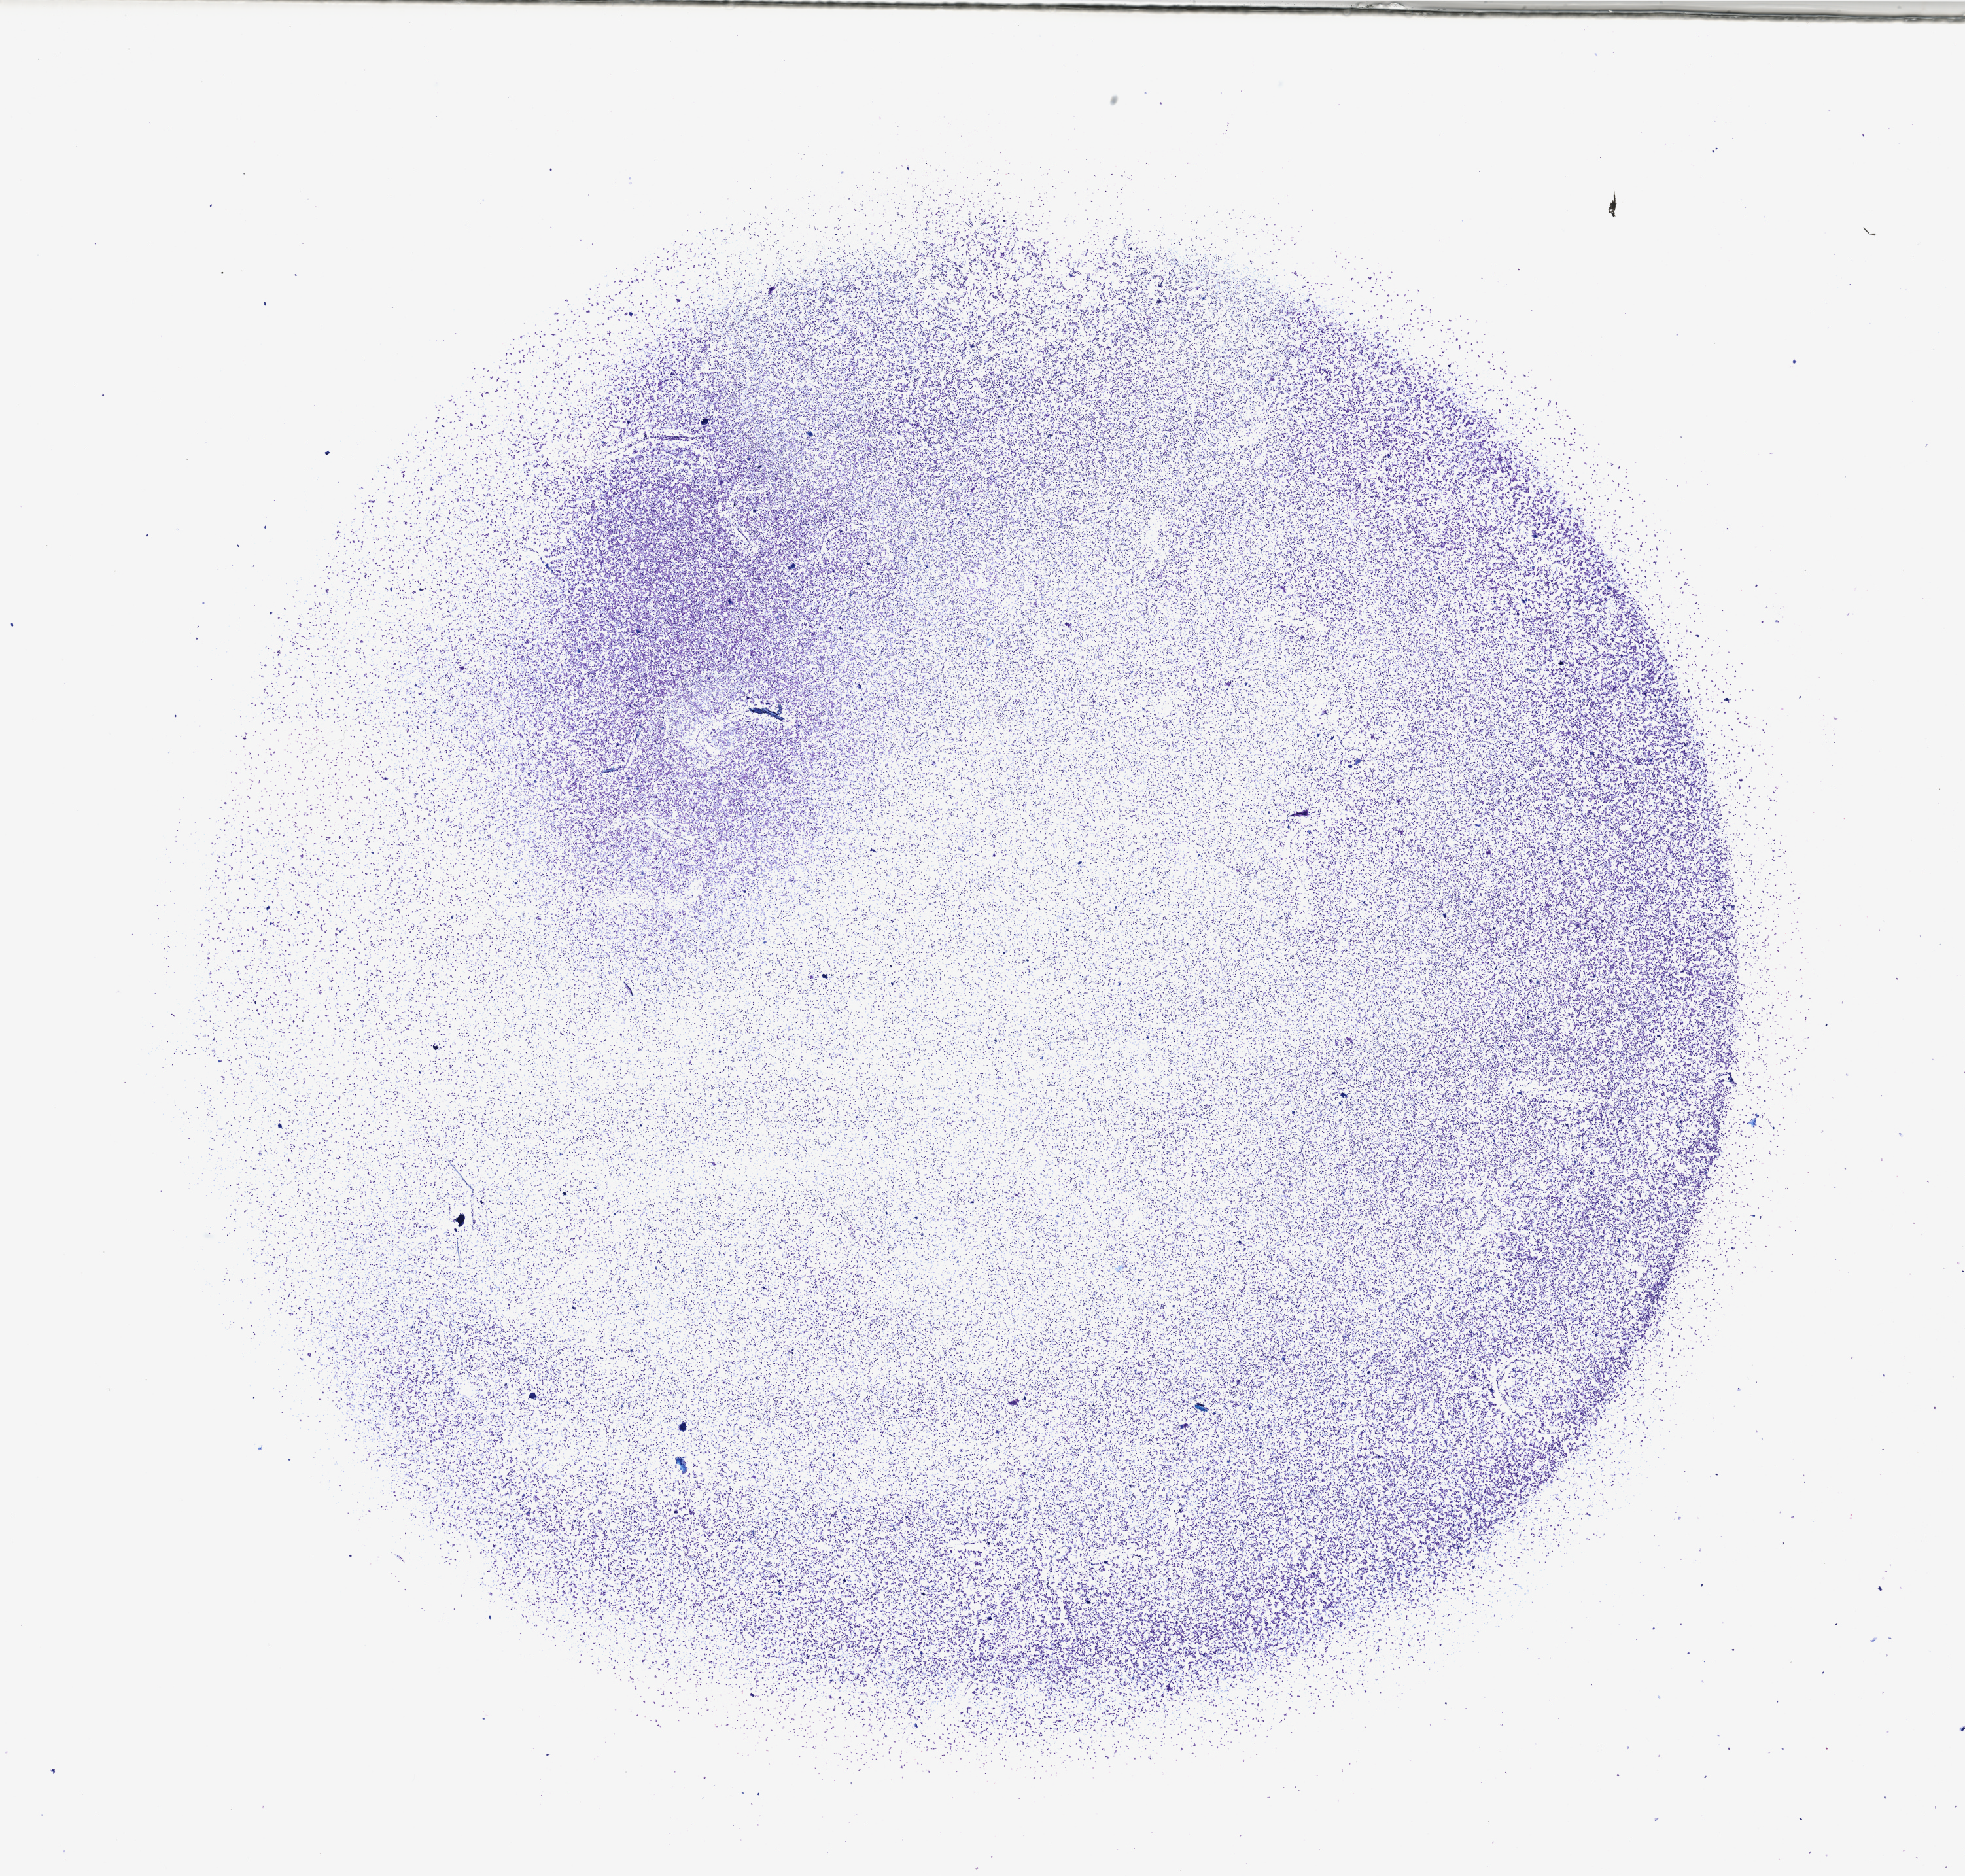
H&E whole-slide image — low-resolution overview of the scanned area, about 23.7 x 22.6 mm (from a 40x scan); bone marrow (leukaemic) sample. Patient: female, age 55 years. Blasts: 90%.
- WHO classification: AML with inv(16)(p13.1q22) or t(16;16)(p13.1;q22); CBFB-MYH11
- diagnosis: Acute Myeloid Leukemia
- FAB classification: M4